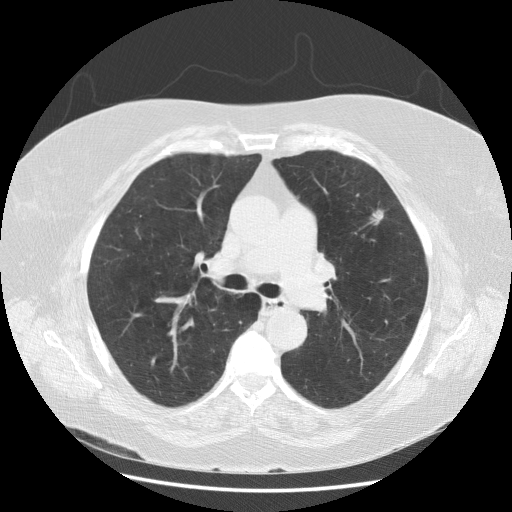
Axial slice from a low-dose chest CT screening exam. Second screening round (one year after baseline). Lung window (W 1500 / L -600 HU). 2.5 mm slice thickness. Standard (soft-tissue) reconstruction kernel (STANDARD). Female participant, aged 68 years at enrolment. Current smoker at enrolment.
• Expert reader's lesion annotation, bounding box <362,204,396,231> (left, top, right, bottom; pixels).
• The screening reader recorded 2 non-calcified nodules or masses ≥4 mm on this exam (left upper lobe, right upper lobe); which of them this box marks is not recorded.
• Official screen result: positive, other.
• Later outcome: lung cancer diagnosed 90 days after this screen — large cell carcinoma, NOS, left upper lobe, undifferentiated (G4), stage IA (AJCC 6th edition), 10 mm at pathology.